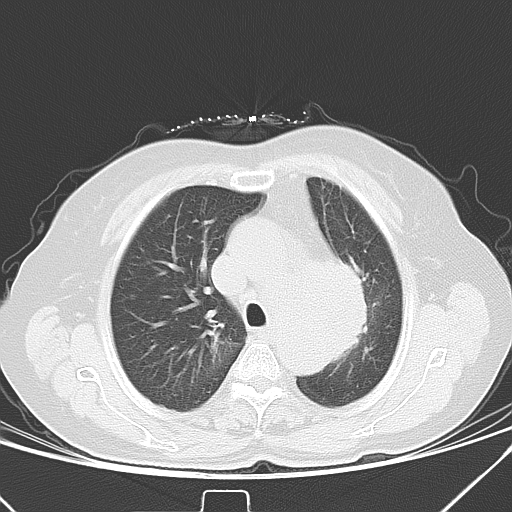
Chest CT, one axial slice. Position 29 of 40 along the scan axis. Lung window (W 1500 / L -600 HU). 5 mm slice thickness. 512 × 512 image matrix, field of view 331 × 331 mm. Female patient, age 59 years. From the clinical record (not read from this slice): clinical TNM (as recorded): T3 N1 M0; histopathological grade: G3.
Outlined on this slice (rectangle marked by the reading radiologist):
- lung tumour (recorded histology: small cell carcinoma): bounding box <334,254,383,374> (left, top, right, bottom; pixels)